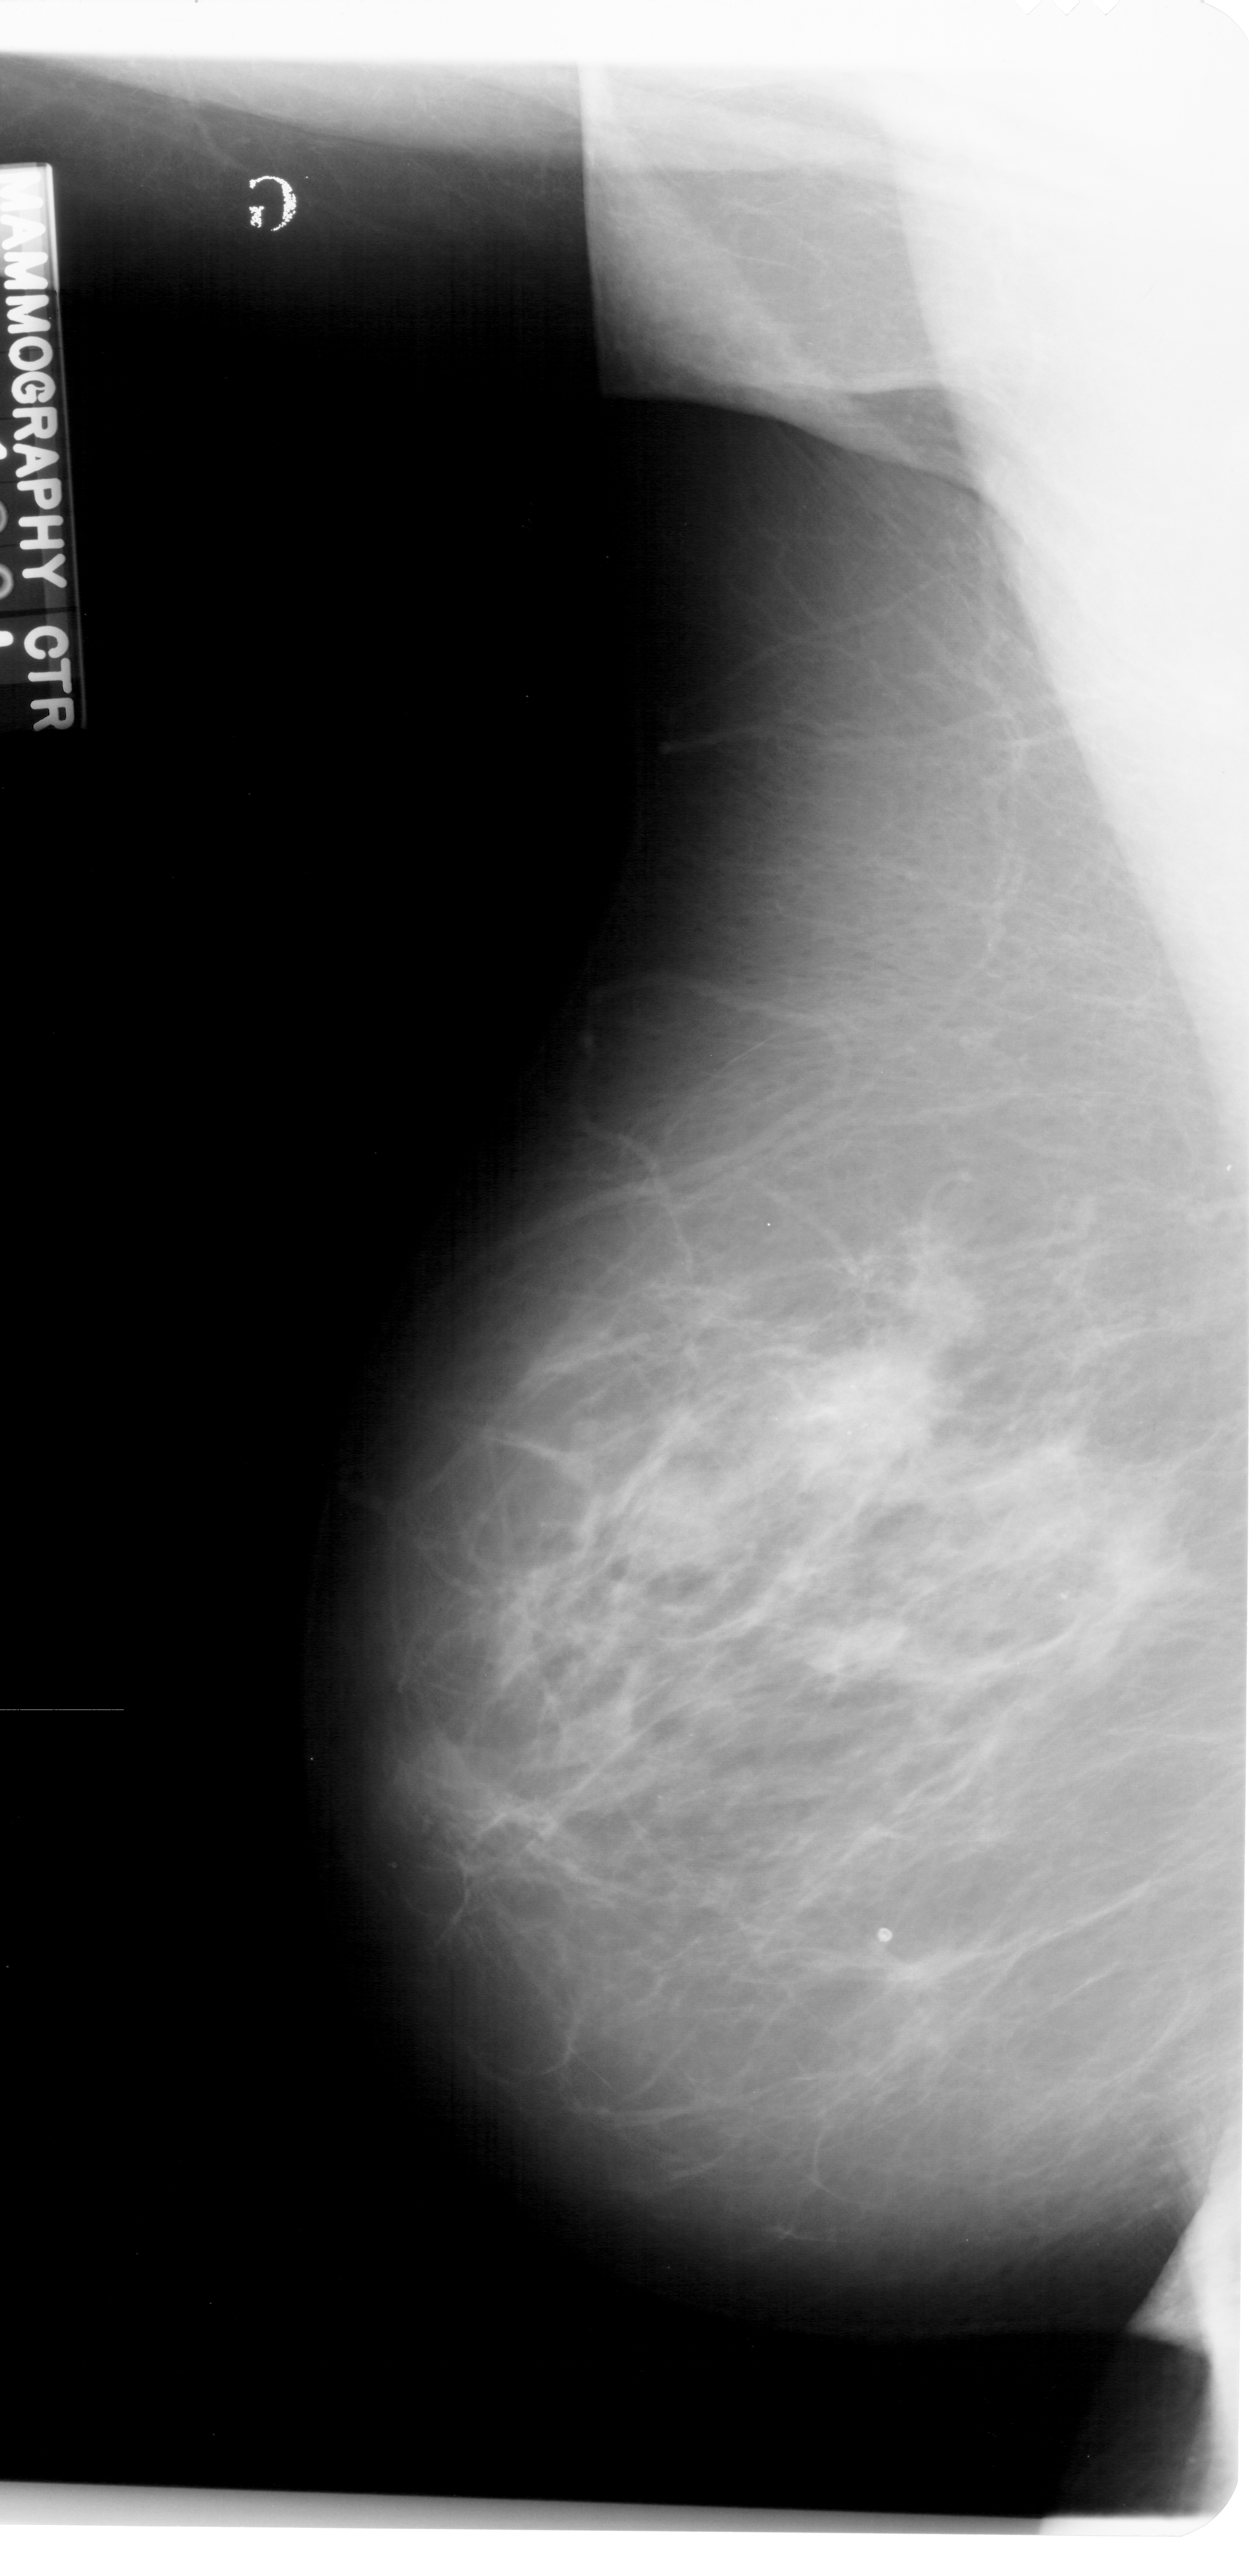
Mammogram (digitized film). Left breast. Mediolateral oblique (MLO) view. Breast composition: heterogeneously dense (BI-RADS density category 3 of 4). 1249 × 2576 image matrix.
Marked abnormalities (boxes around the expert regions of interest):
- mass, shape irregular, margins spiculated; BI-RADS assessment category 5; pathology (as recorded): malignant: box from (x=793, y=1347) to (x=931, y=1474) px